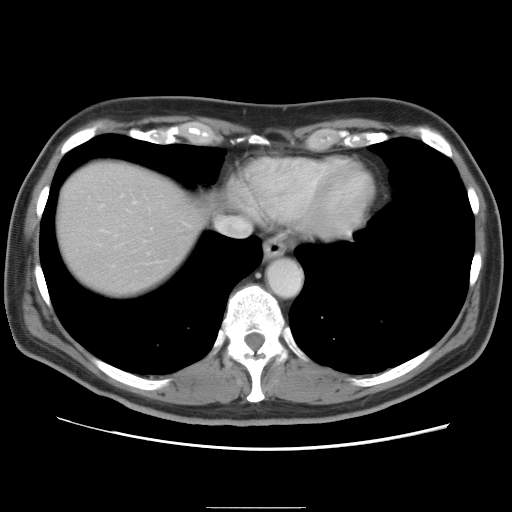
Contrast-enhanced abdominal CT, one axial slice. Position 75 of 87 along the scan axis. Intravenous contrast given. Soft-tissue window (W 400 / L 40 HU). 5 mm slice thickness. 512 × 512 image matrix, field of view 363 × 363 mm. Male patient, age 63 years. Case-level facts recorded for this patient, not image findings: diagnosis: colorectal cancer liver metastases, imaged before liver resection; multiple liver metastases: no; largest metastasis: 9 cm; disease in both lobes: no.
Structures marked on this image (manually delineated by an expert):
- hepatic veins: bounding box [x1, y1, x2, y2] px = [98, 200, 245, 237]
- liver: [56, 161, 198, 299]
- planned liver remnant (the part of the liver to remain after resection): [57, 177, 196, 298]
- portal vein (with intrahepatic branches): [96, 193, 153, 267]